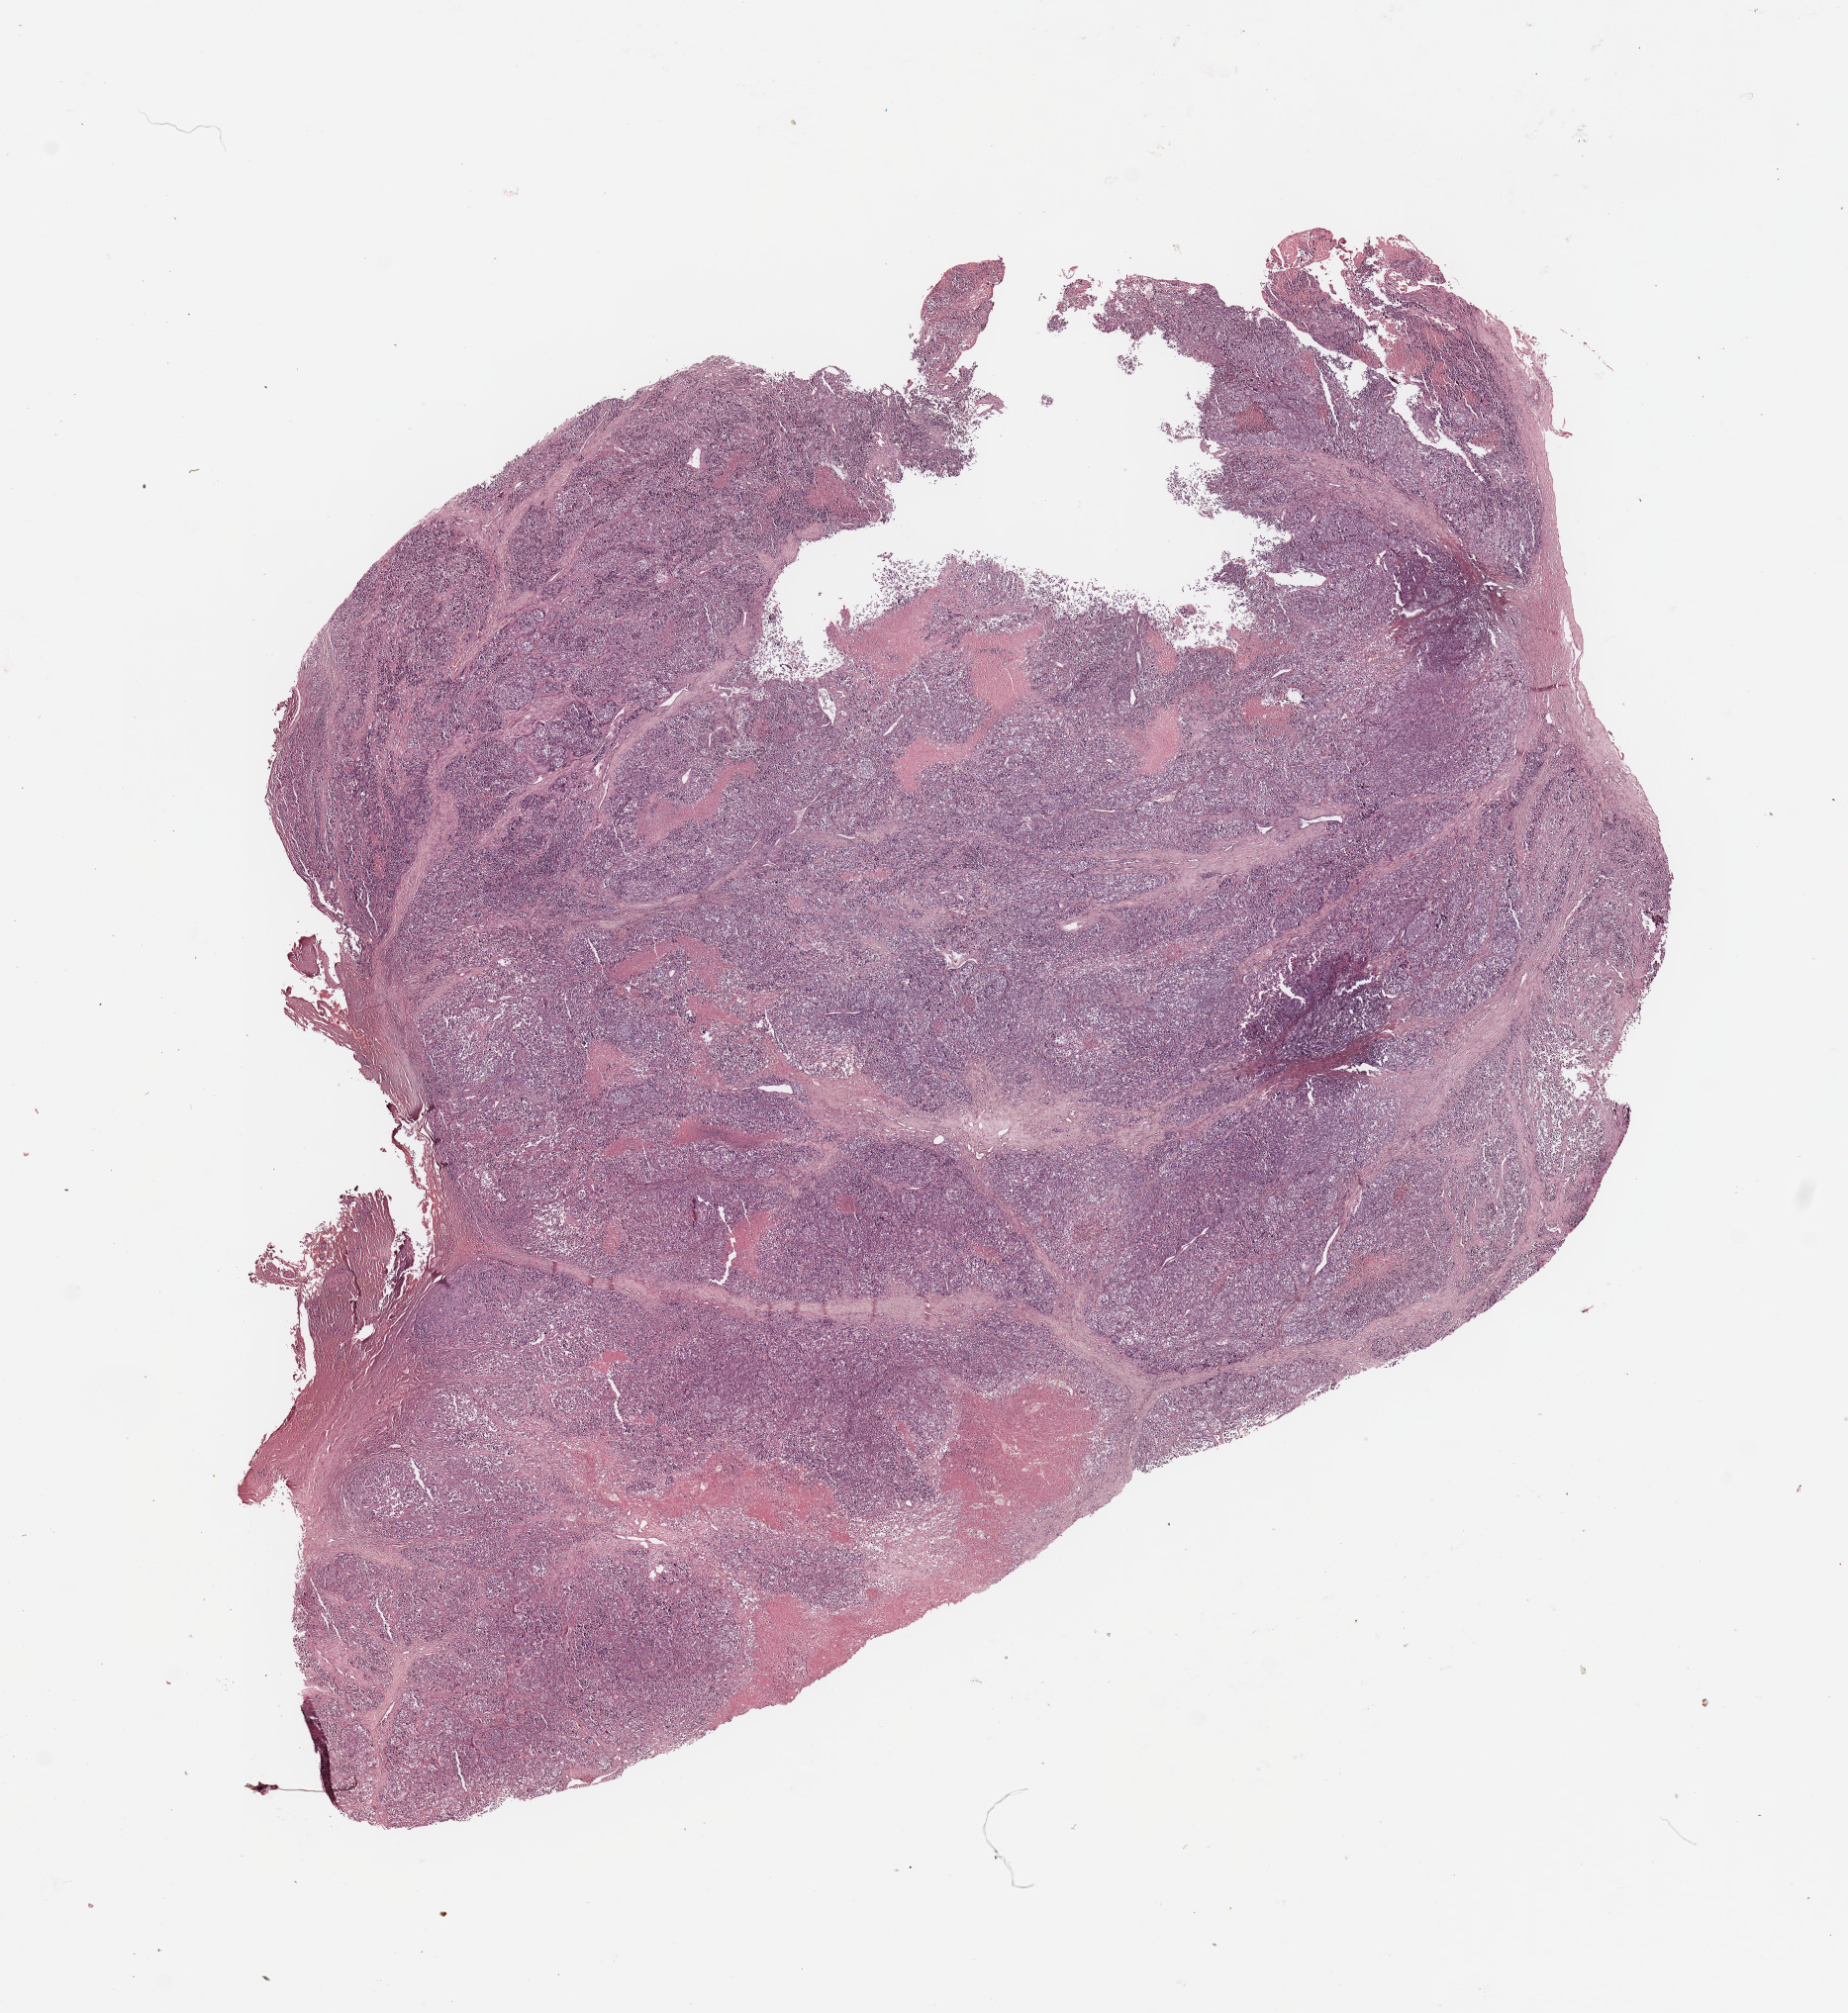
Whole-slide histology image, Hematoxylin and eosin (H&E) stained, whole scanned area (about 14.8 x 16.1 mm, from a 20x scan) shown as a low-resolution overview; melanoma tumour tissue; sampled site not recorded. Patient: male, age 76 years.
Histologic diagnosis: Malignant melanoma, NOS. AJCC pathologic stage: IIA. Primary tumour site (as recorded): trunk.